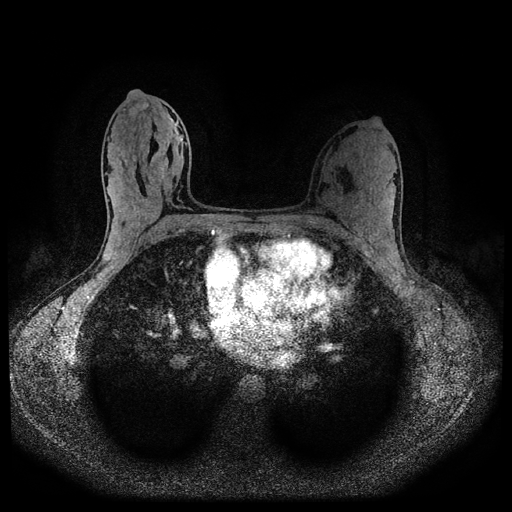
Breast MRI (dynamic contrast-enhanced, multi-phase), one axial slice; position 58 of 116 along the scan axis; dynamic contrast-enhanced series, time point 2 of 5 at this slice position (early post-contrast); 1.5 T; TE 2.7 ms, TR 5.4 ms; 512 × 512 image matrix, field of view 330 × 330 mm. Female patient, age 32 years.
Outlined on this slice (semi-automatic segmentation, software-assisted and operator-edited):
- breast lesion (labelled benign in the annotation): bounding box (x1, y1, x2, y2) in pixels: (129, 103, 152, 117)